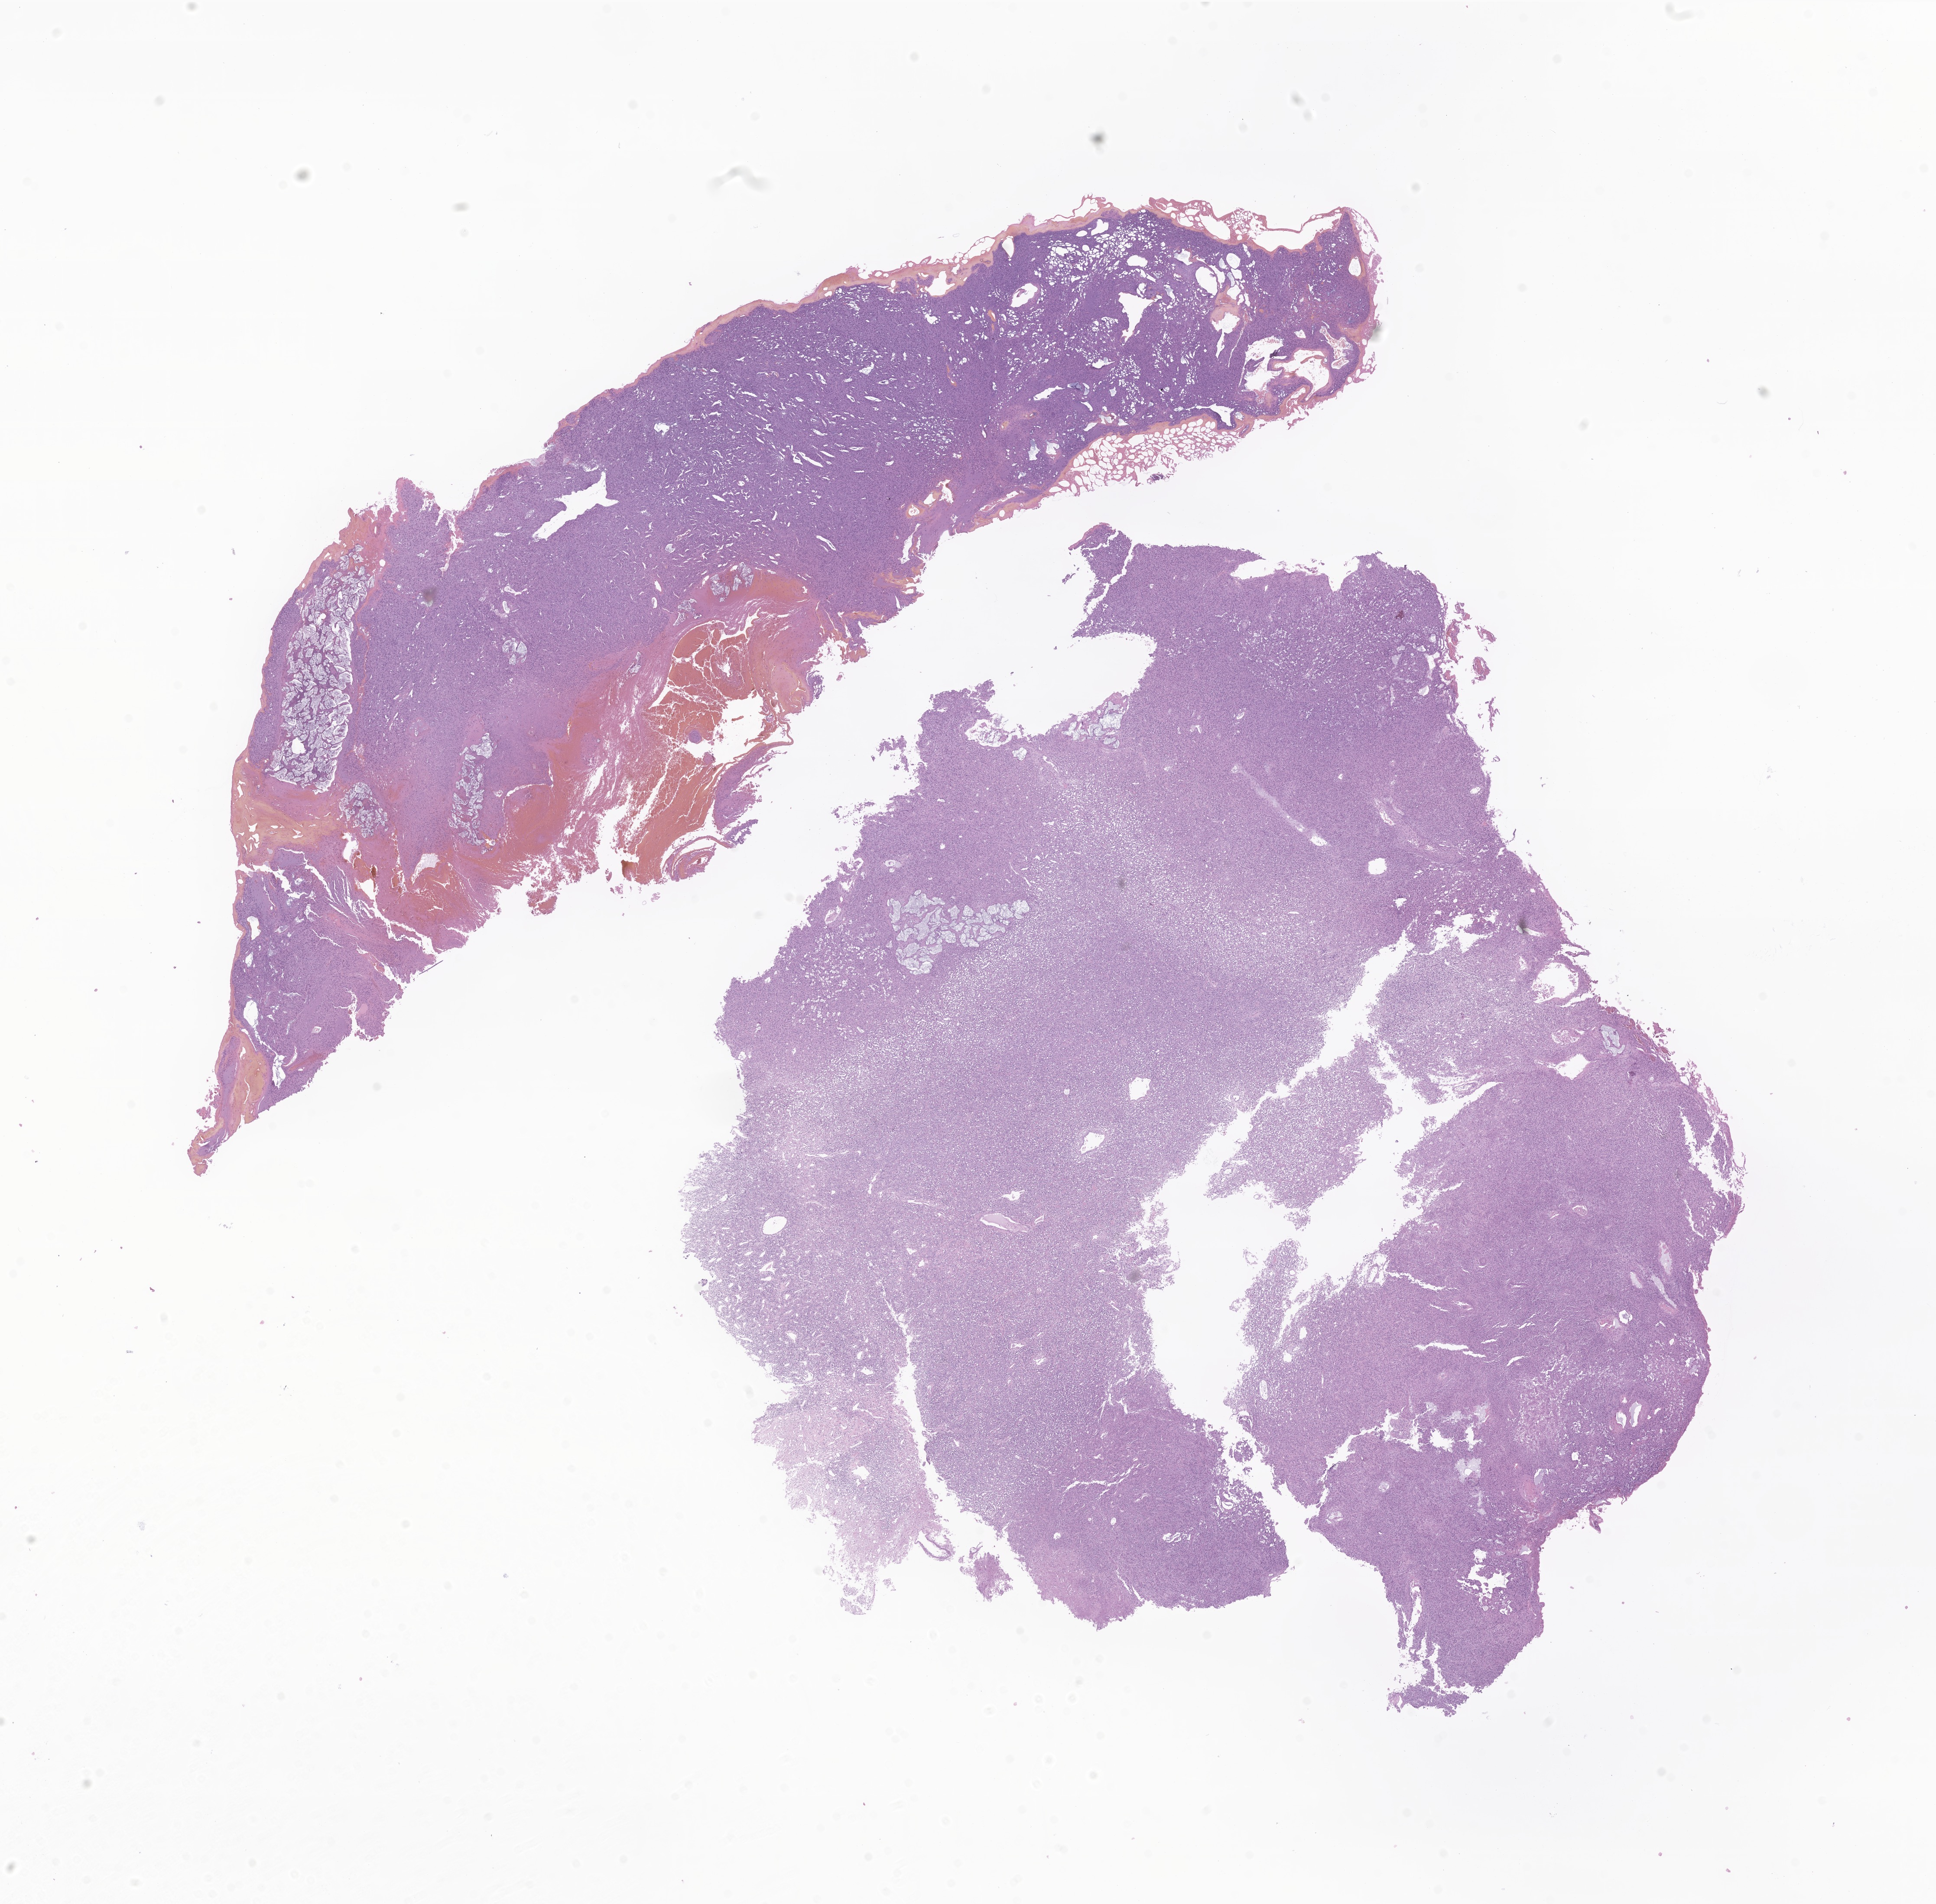
Digitized hematoxylin and eosin (H&E)-stained section of tumor tissue from the brain, a low-resolution overview of the entire scanned area, about 18.8 x 18.5 mm, FFPE section. Female patient, age 206 months (17 years 2 months).
Diagnosis: Solitary fibrous tumor/Hemangiopericytoma, grade 1.